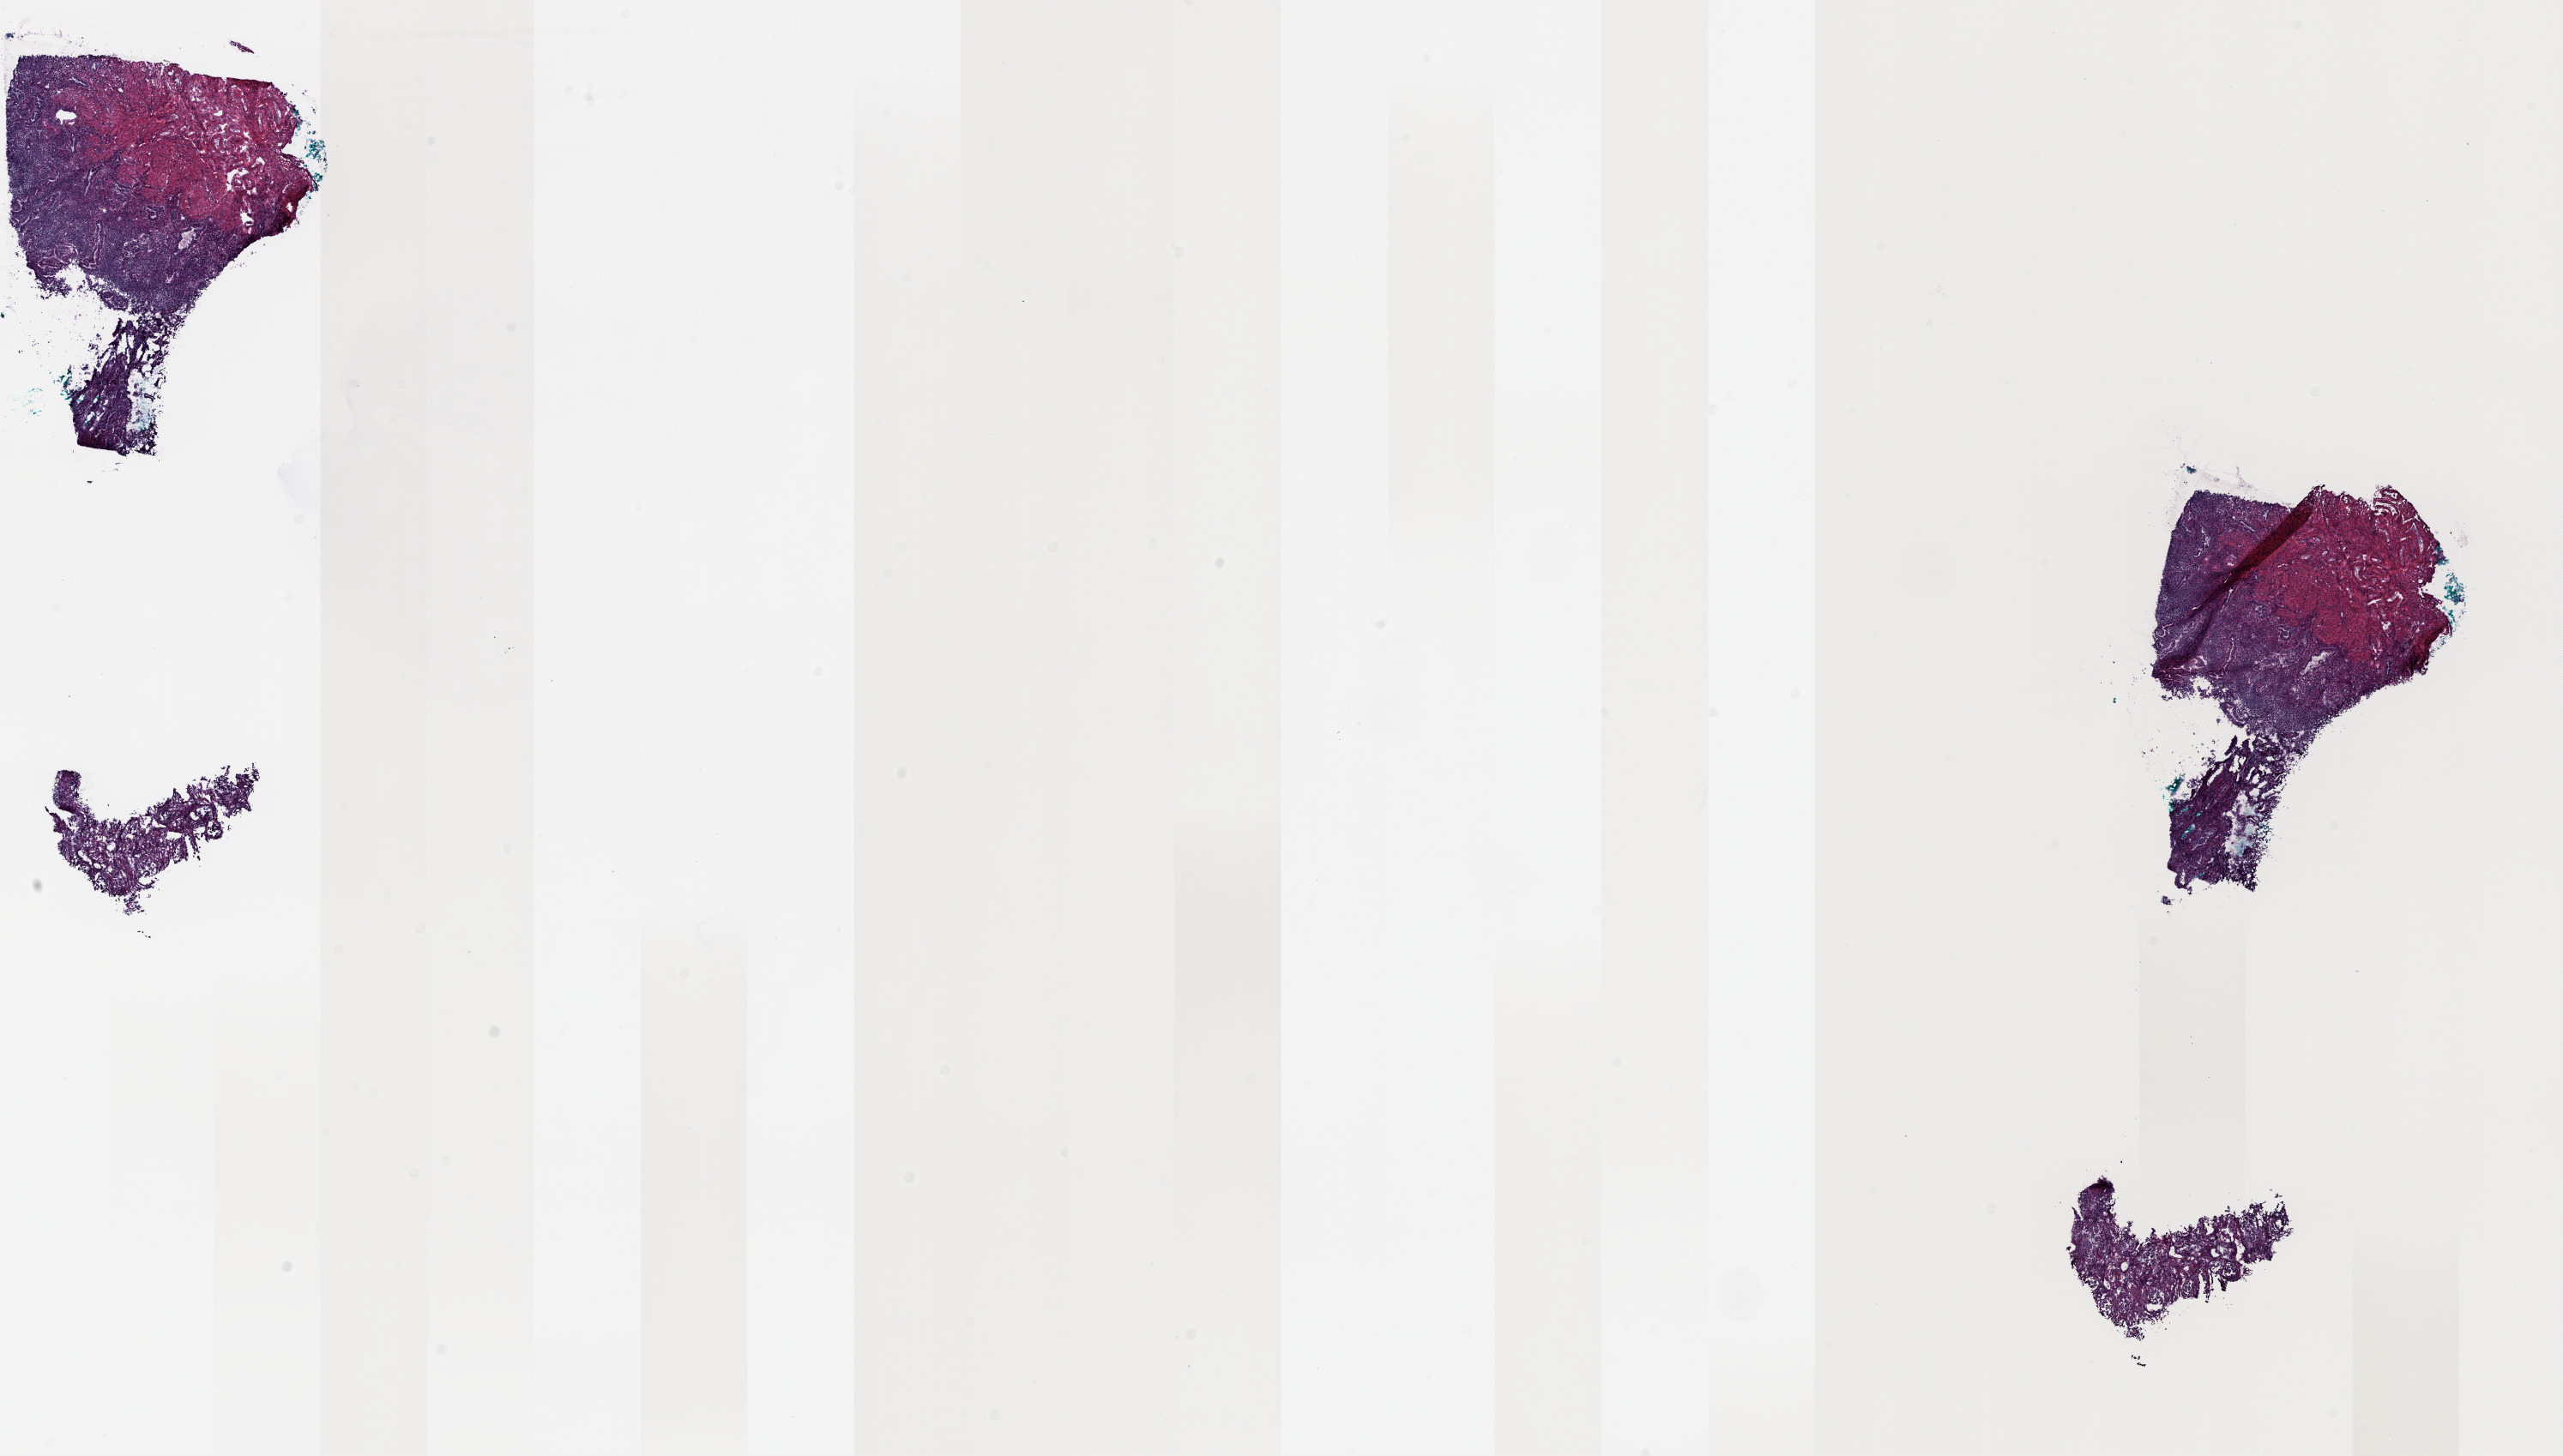
Hematoxylin and eosin (H&E) stained whole-slide image — low-resolution overview of the scanned area, about 23.7 x 13.5 mm (acquisition: 20x scan), frozen section from the top of the tissue portion, sample: solid tissue normal (non-tumour tissue), uterus.
This section: solid tissue normal (non-tumour) sample.